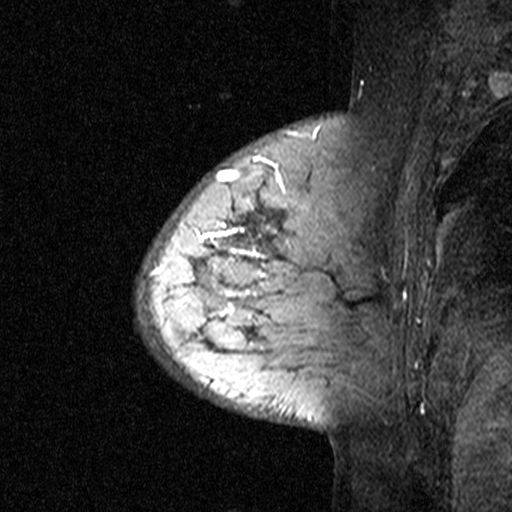
Breast MRI (dynamic contrast-enhanced), one sagittal slice. Position 10 of 44 along the scan axis. Dynamic contrast-enhanced study with each time point stored as its own series, time point 3 of 4 at this slice position (ordered by acquisition time). 1.5 T. TE 4.5 ms, TR 11 ms. 3 mm slice thickness. 512 × 512 image matrix. Patient: female, 65 years. From the clinical record (not read from this slice): setting: breast cancer imaged before/during neoadjuvant chemotherapy; receptor status: HER2-positive.
Structures marked on this image (semi-automatically segmented with operator editing):
- analysis volume of interest (the breast-tissue region the enhancement analysis was run in; not a lesion): bounding box <182,190,353,361> (left, top, right, bottom; pixels)
- tumour enhancement mask (voxels above the 90 % enhancement threshold inside the analysis volume of interest): <202,218,267,316>